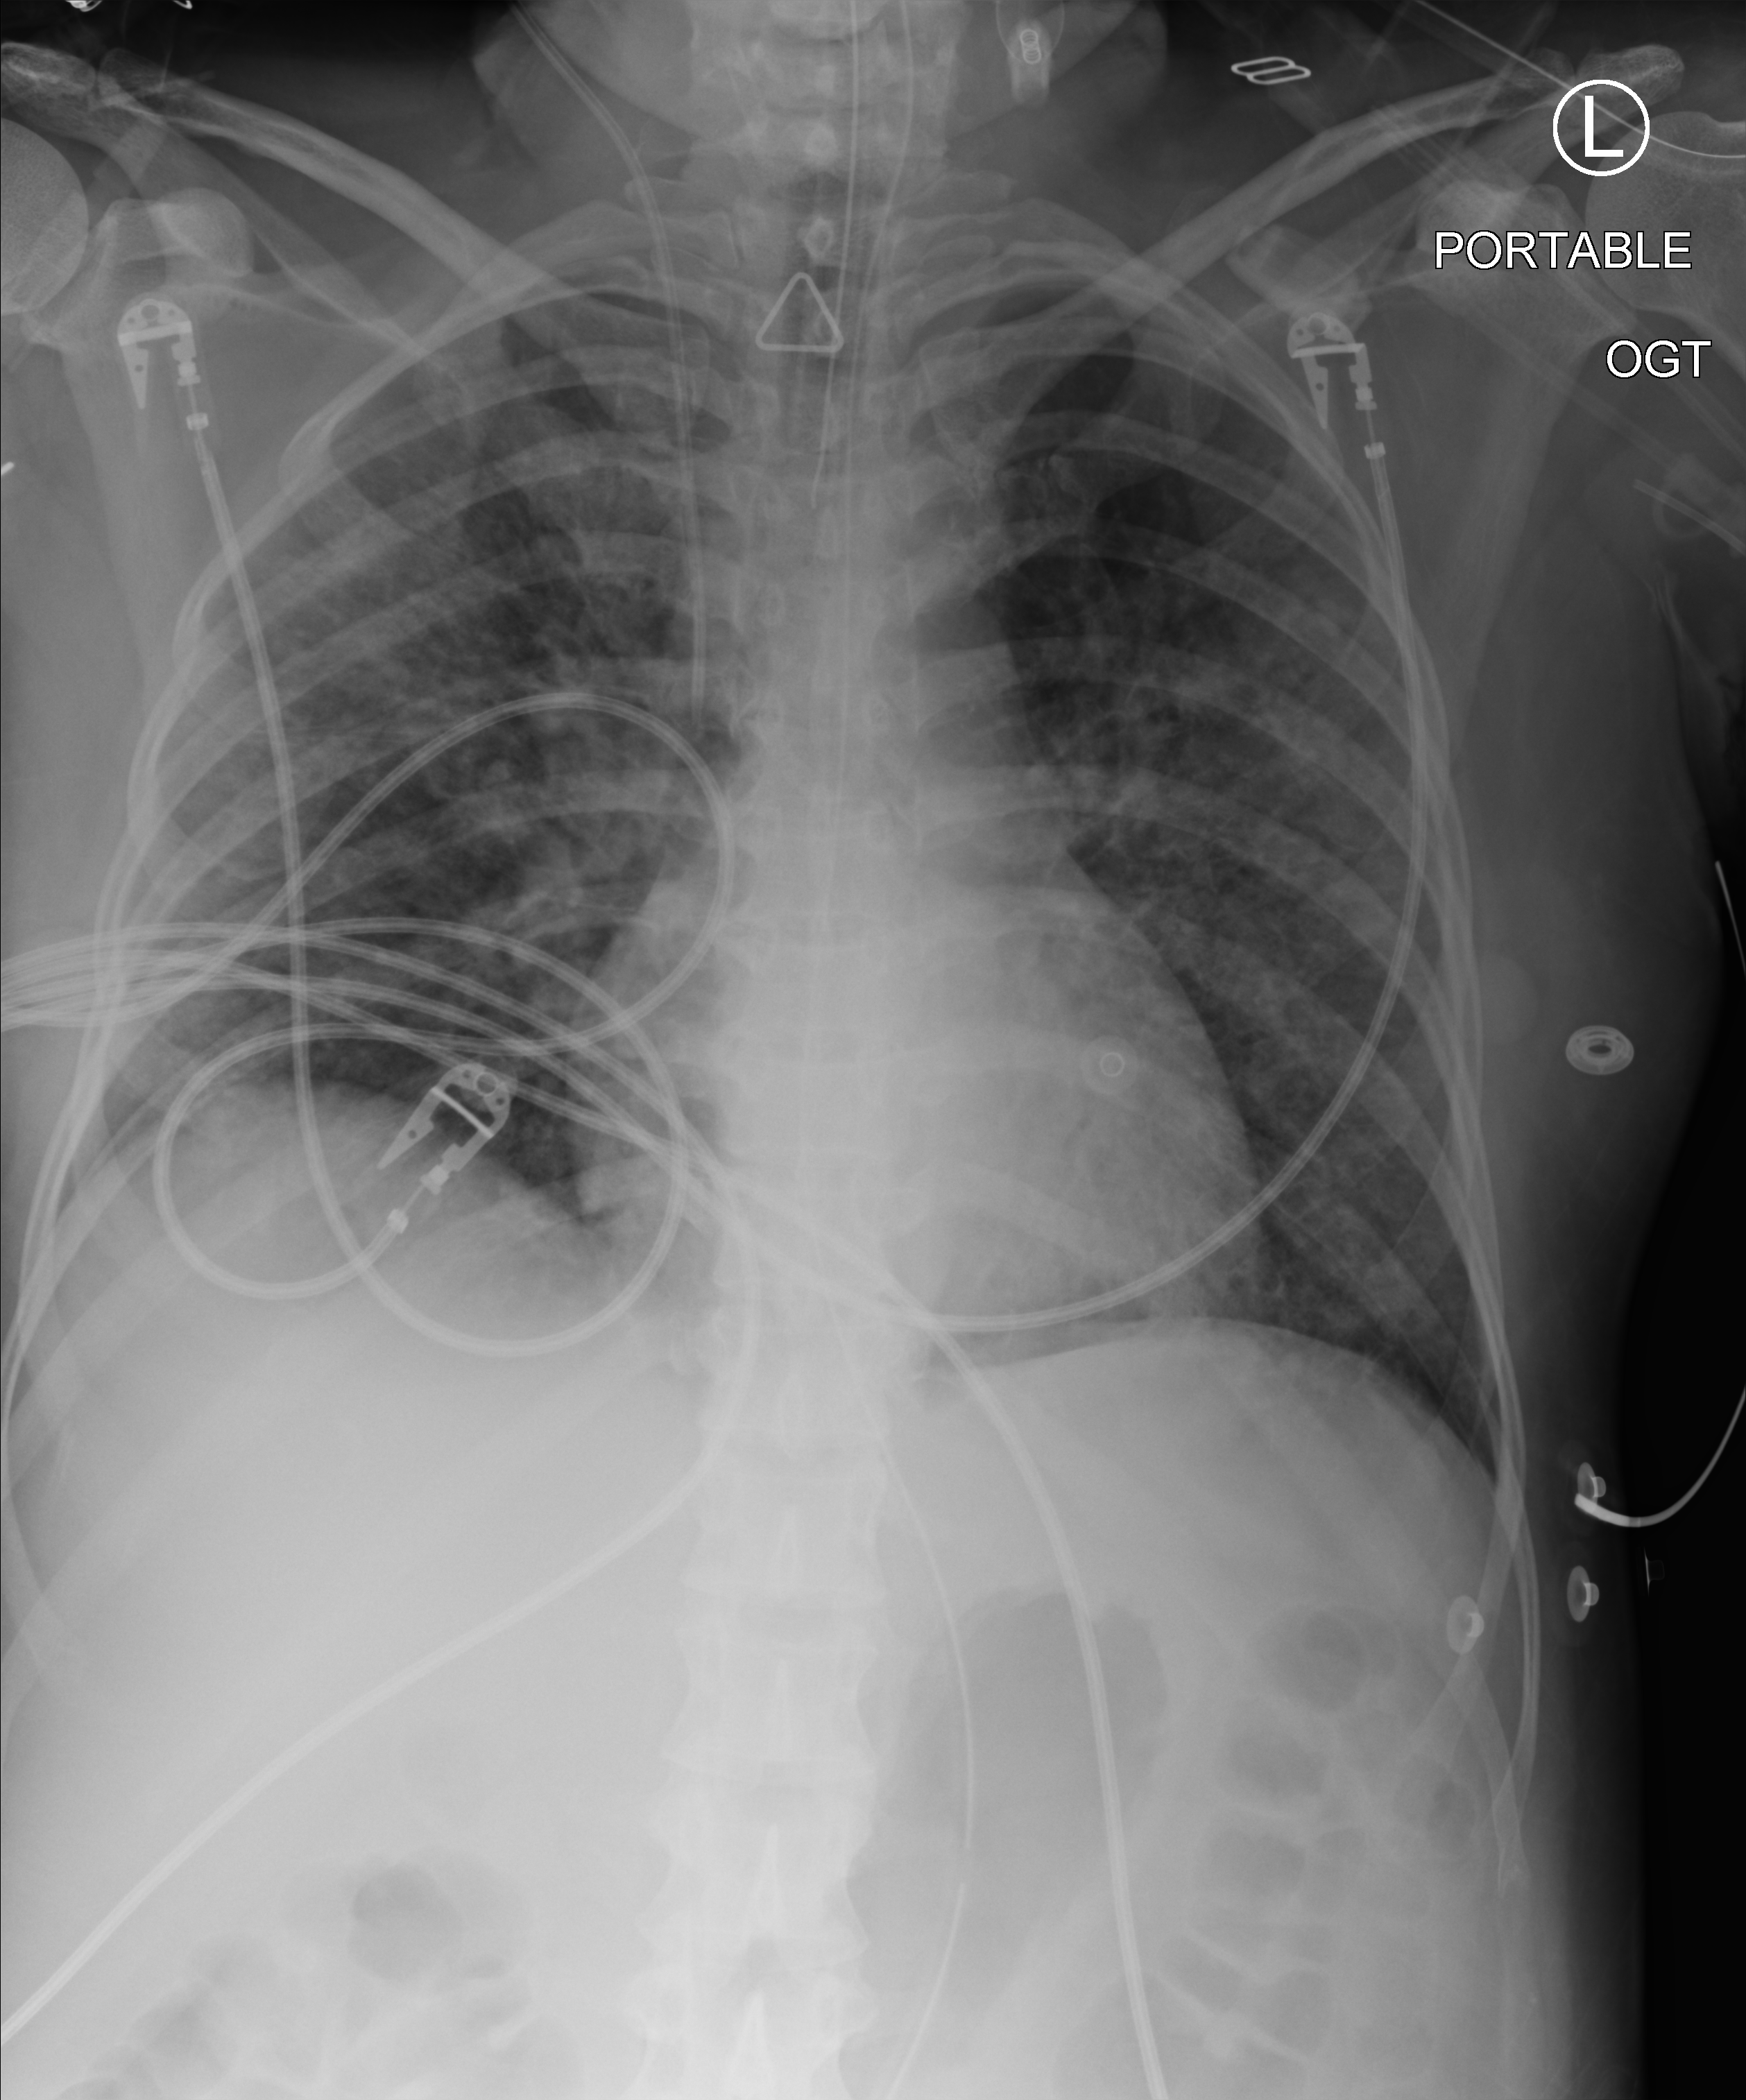
Portable chest radiograph; anteroposterior (AP) projection. Female patient hospitalised with COVID-19, age 18–59 years.
From the hospital-stay record, not from the radiograph (when in the stay this image was taken is not recorded): length of hospital stay: 71 days; admitted to intensive care during this hospital stay: yes; mechanically ventilated during this hospital stay: yes.